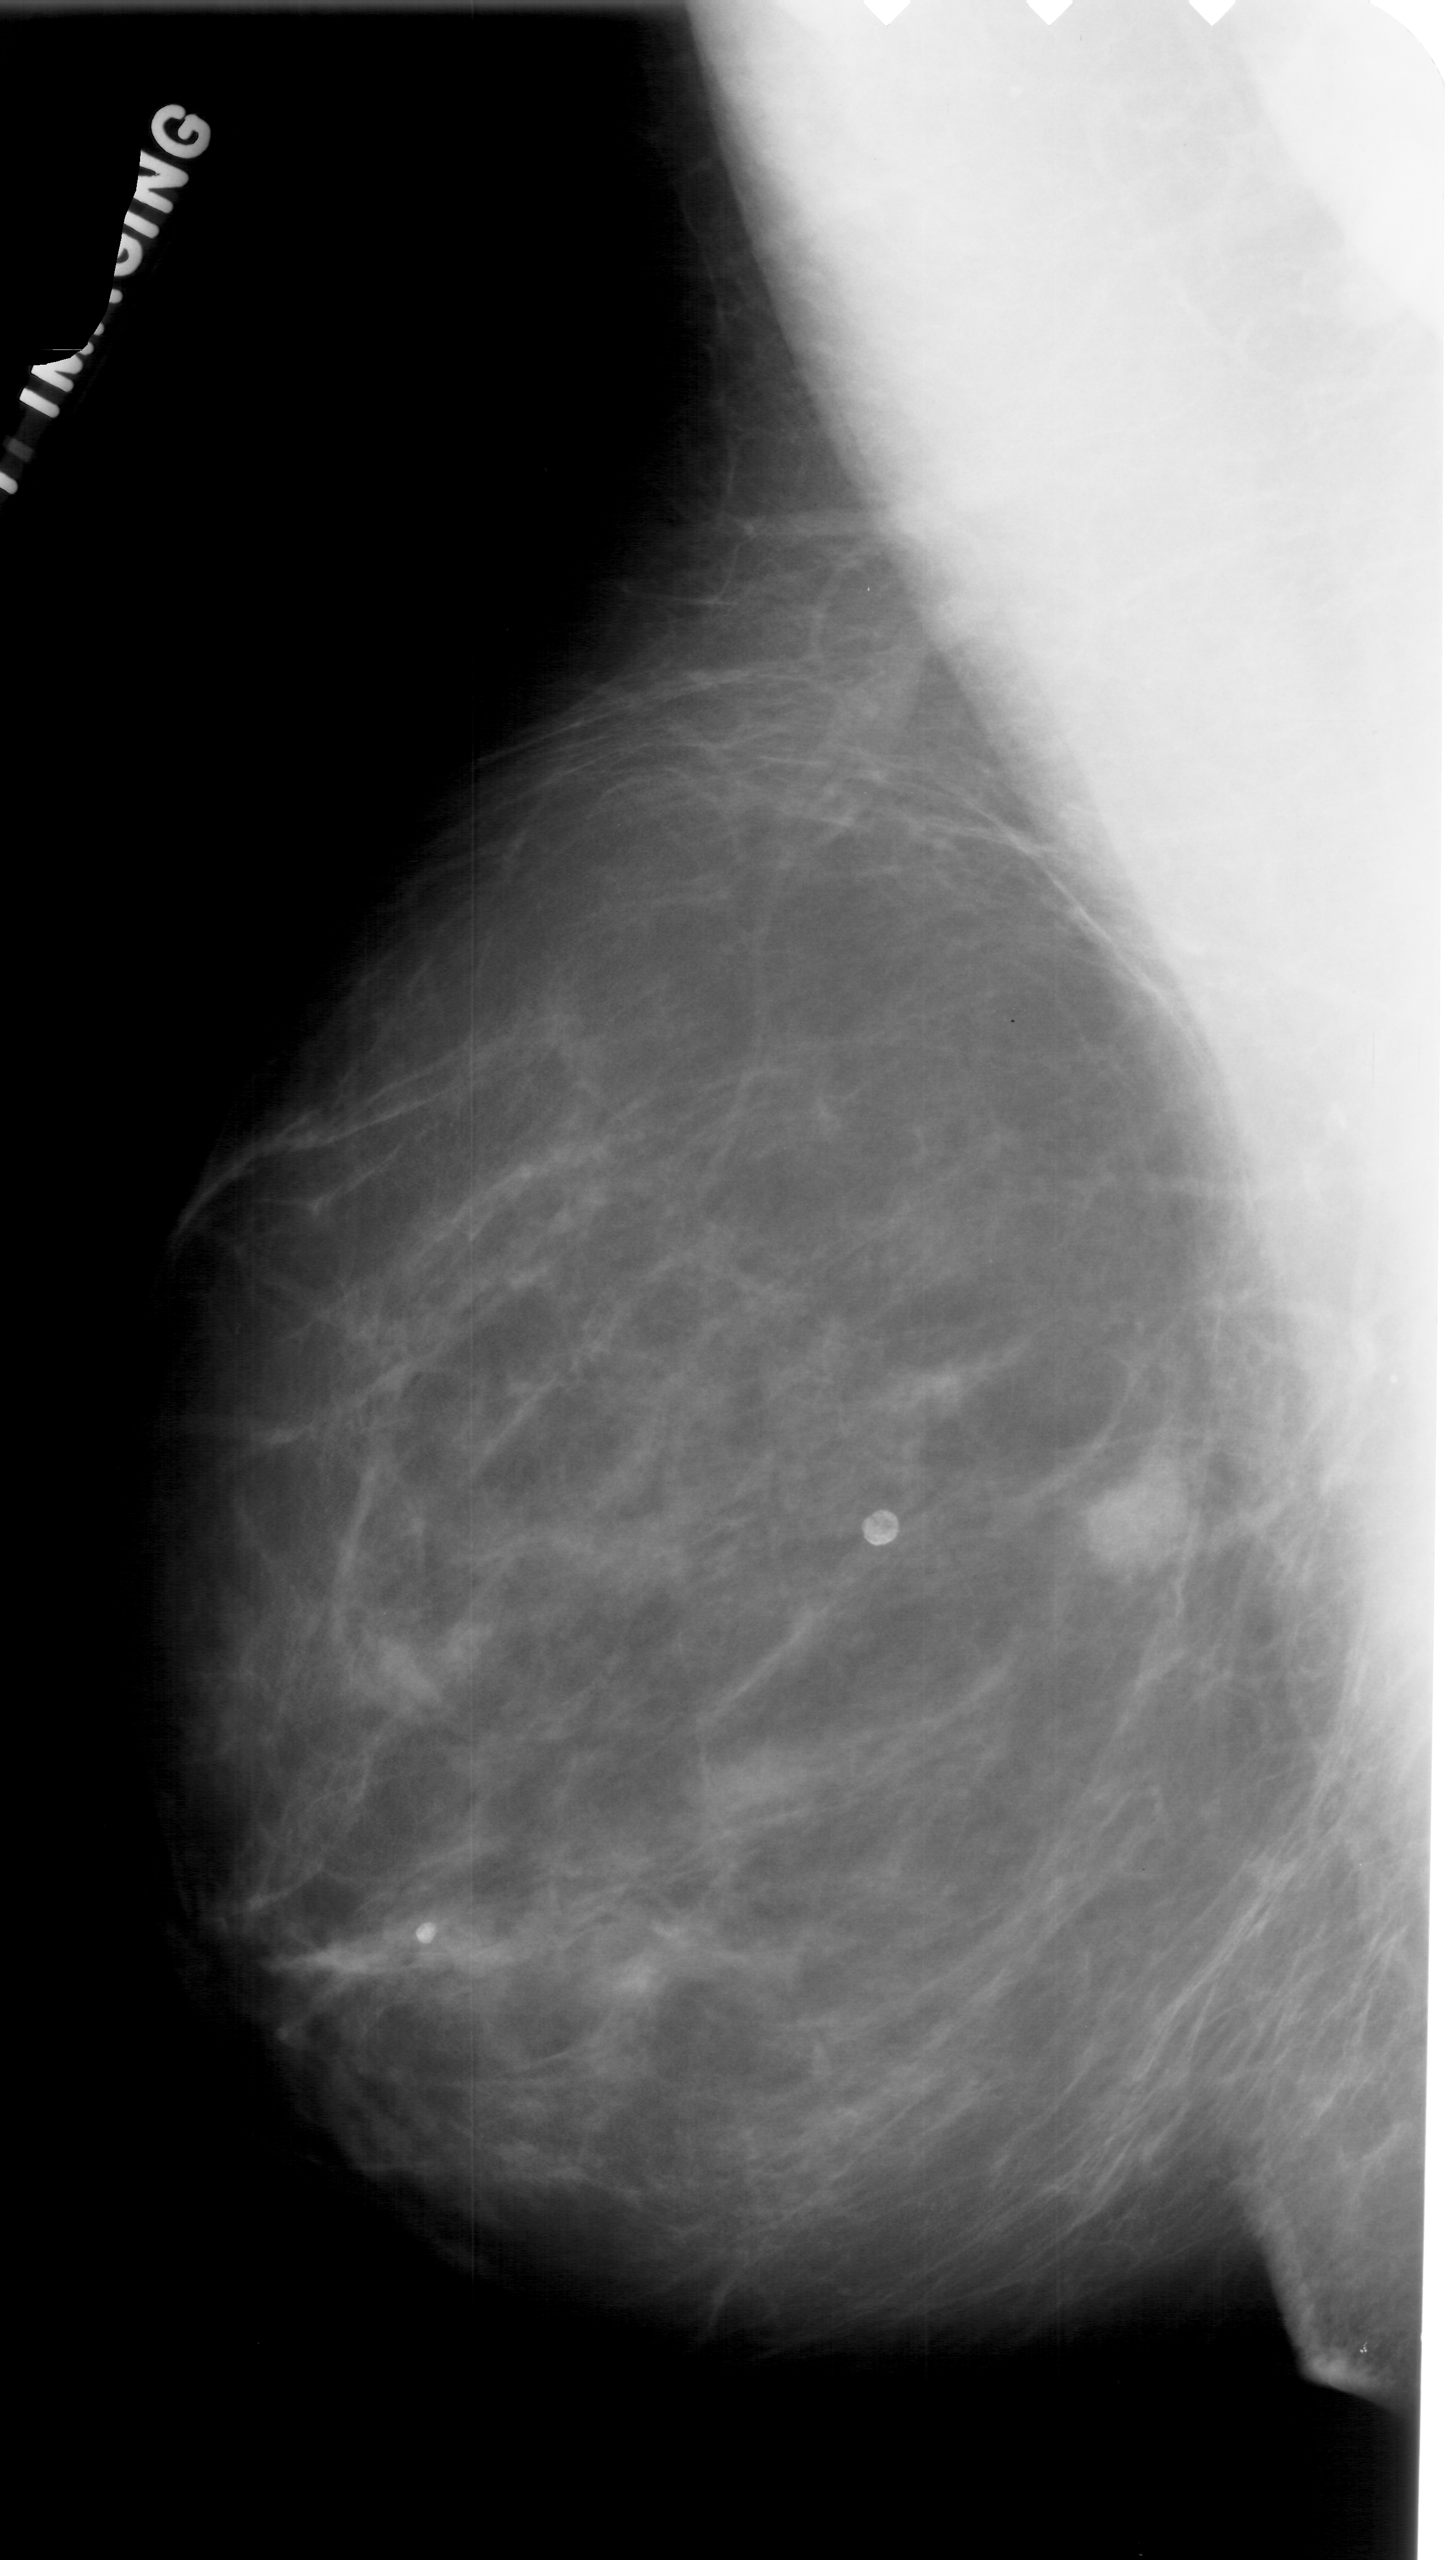
Mammogram (digitized film); left breast; MLO view; BI-RADS breast density category 2 (scale 1–4).
- Abnormality record for this image: mass, shape lobulated, margins obscured; BI-RADS assessment category 4; subtlety rating 5 on a 1 (subtle) to 5 (obvious) scale; pathology (as recorded): benign.